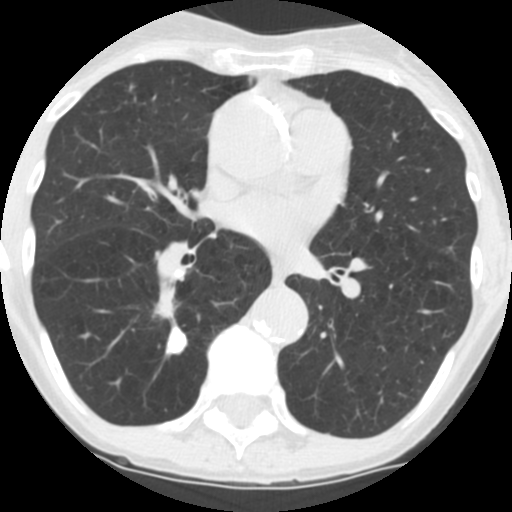
Low-dose screening chest CT, one axial slice; position 61 of 124 along the scan axis; reconstruction kernel STANDARD; 120 kVp; lung window (W 1500 / L -600 HU); 512 × 512 image matrix.
Annotated regions visible in this slice (manually delineated by an expert):
- lesion 1 (tumor, lower lobe of right lung): bounding box [x1, y1, x2, y2] px = [159, 301, 175, 317]